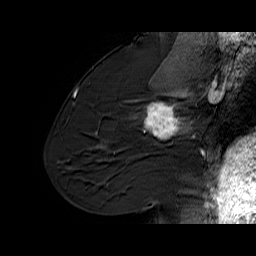
Breast MRI (dynamic contrast-enhanced), one sagittal slice; slice 35 of 60 in the series (ordered by position); dynamic contrast-enhanced series, time point 2 of 6 at this slice position (early post-contrast); 1.5 T; TE 6.1 ms, TR 32.9 ms; 4 mm slice thickness; 256 × 256 image matrix. Female patient. From the clinical record (not read from this slice): setting: breast cancer imaged before/during neoadjuvant chemotherapy; receptor status: HER2-positive.
Outlined on this slice (semi-automatic segmentation, software-assisted and operator-edited):
- analysis volume of interest (the breast-tissue region the enhancement analysis was run in; not a lesion): box from (x=127, y=95) to (x=194, y=165) px
- tumour enhancement mask (voxels above the 100 % enhancement threshold inside the analysis volume of interest): (x=144, y=95)–(x=190, y=138)